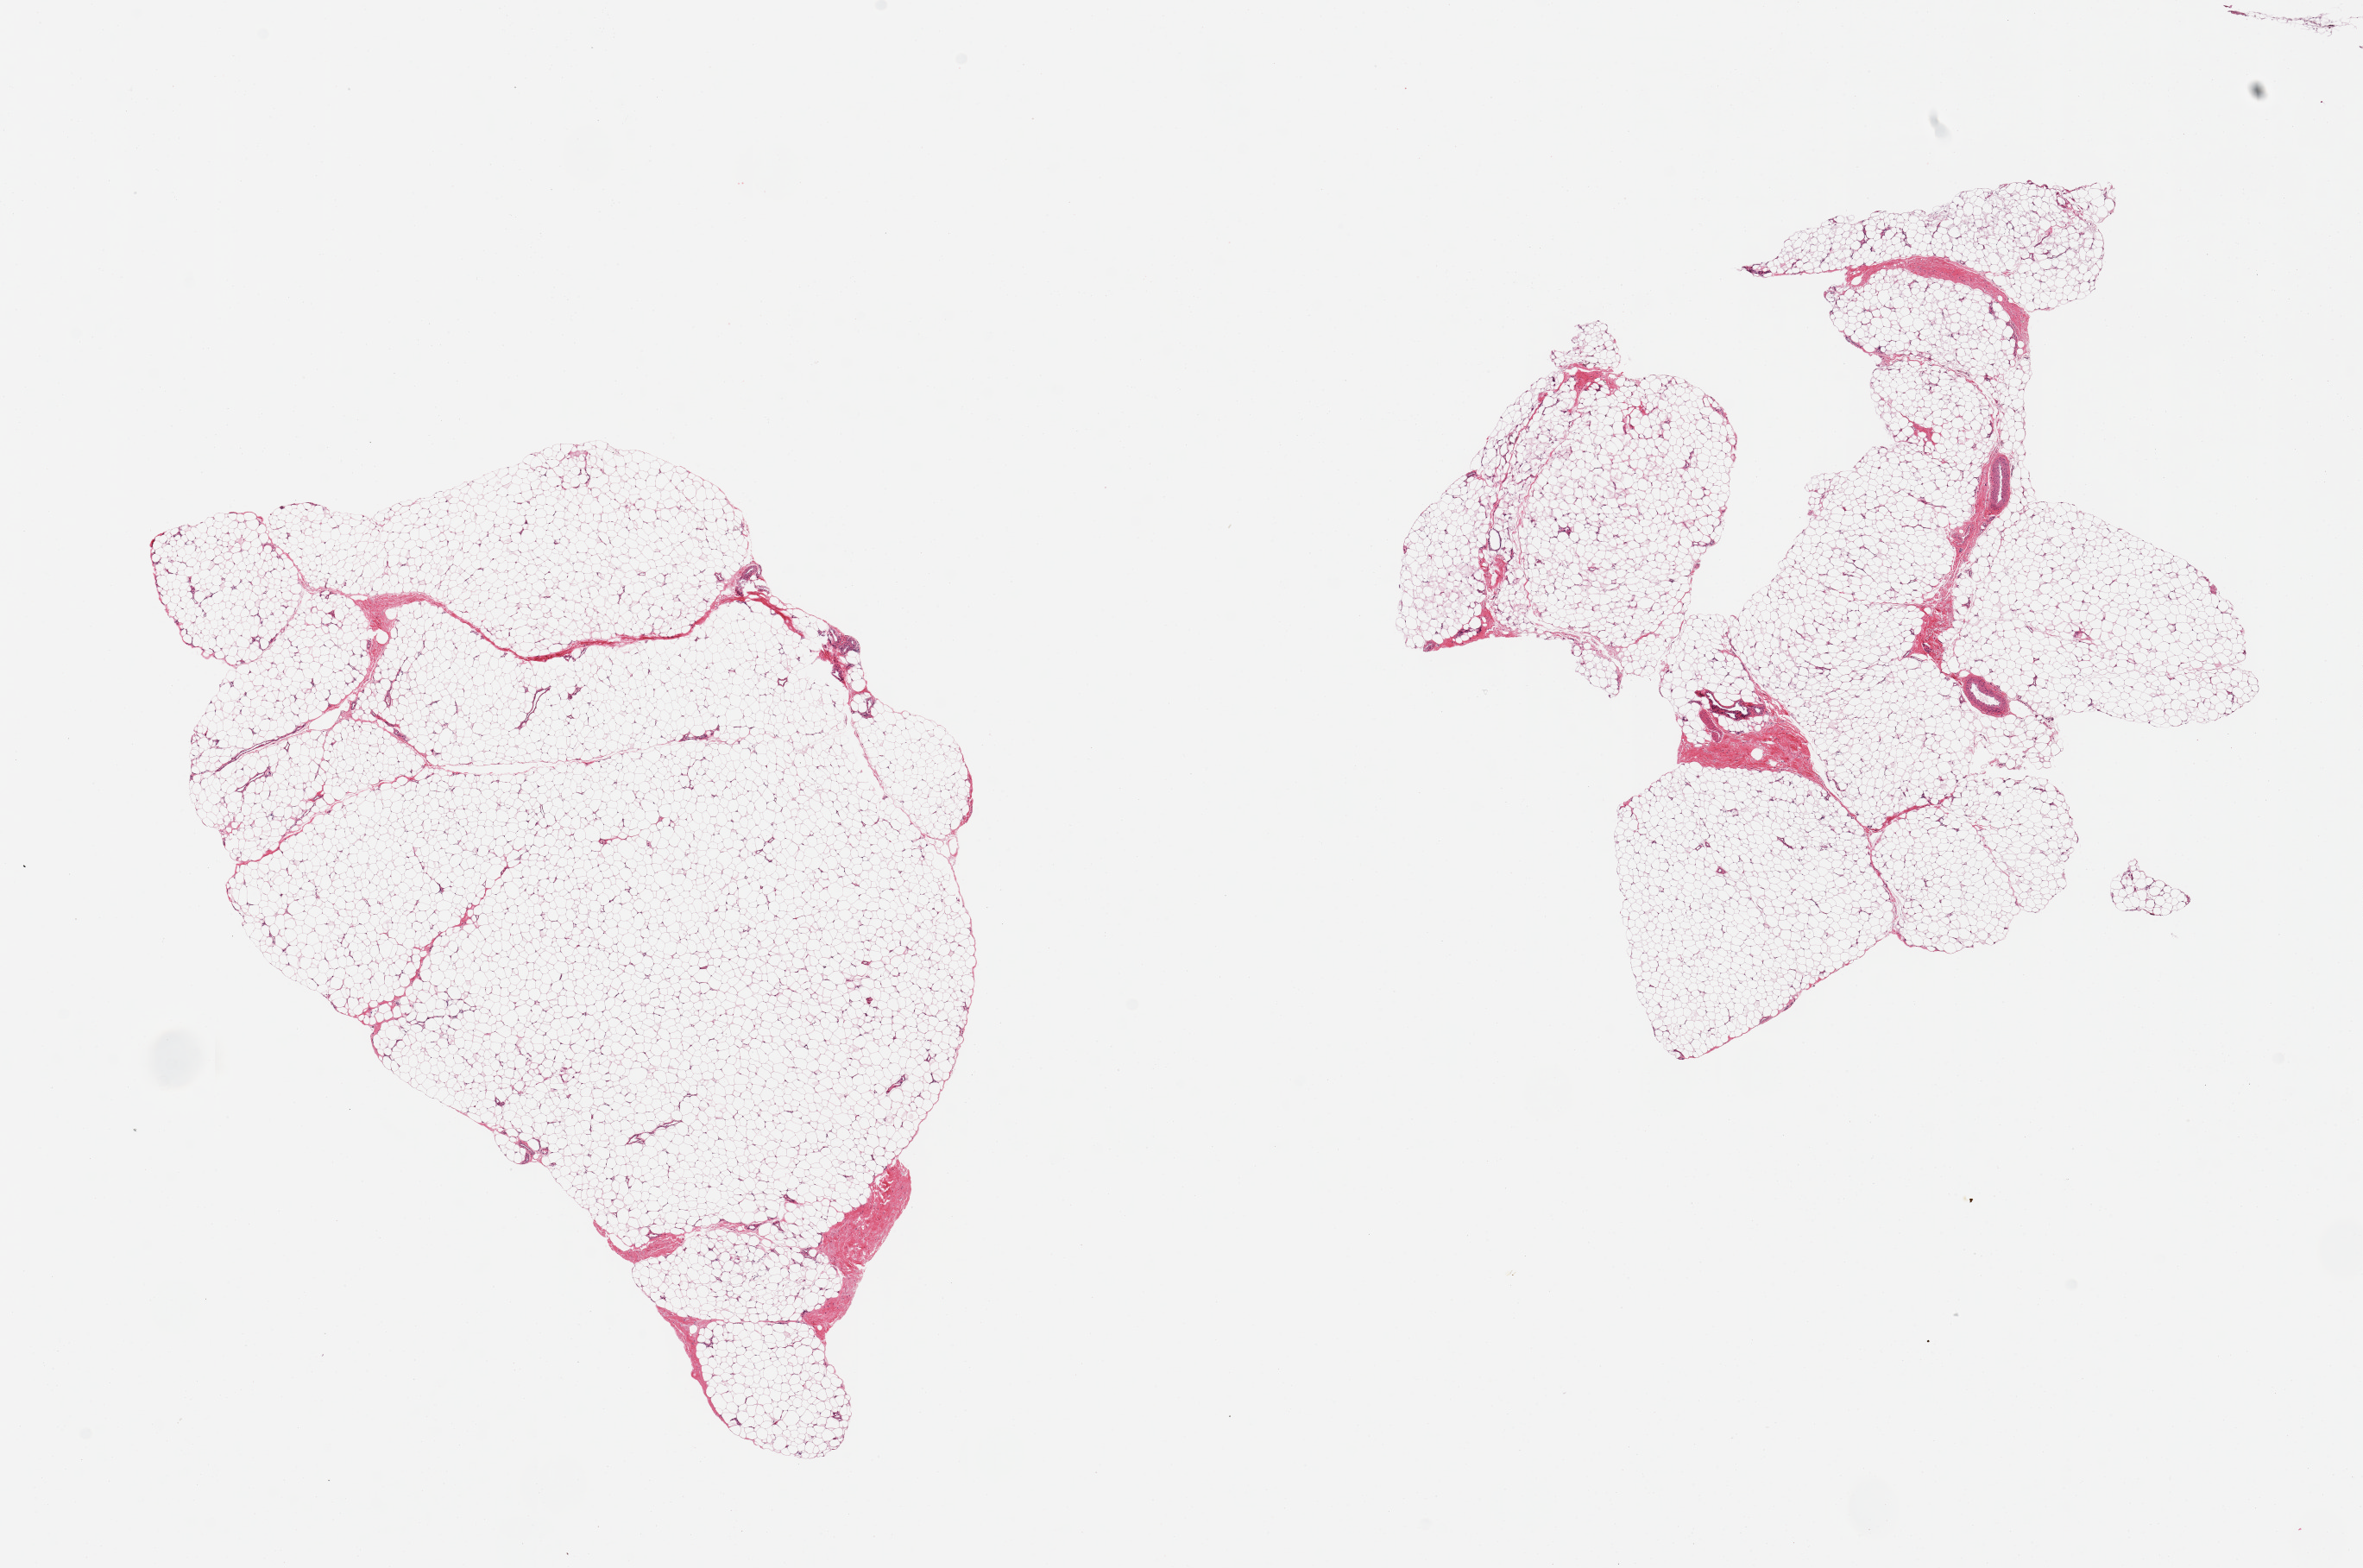
Haematoxylin and eosin whole-slide image — low-resolution overview of the scanned area, about 21.7 x 14.4 mm (acquisition: 20x scan), PAXgene-fixed, paraffin-embedded tissue, sampled site (target tissue): adipose tissue, donor tissue sample. Female donor.
Reviewer comment on this tissue sample: 2 pieces, ~10% fascial/vasuclar tissue.